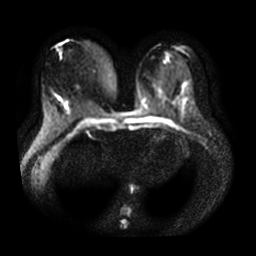
Breast MRI, one axial slice; position 17 of 35 along the scan axis; diffusion-weighted series; image 2 of 4 stored at this slice position (different b-values; order by instance number); 3 T; 5 mm slice thickness; 256 × 256 image matrix. Female patient.
Structures marked on this image (expert manual segmentation):
- tumour on diffusion-weighted imaging: box from (x=64, y=103) to (x=68, y=109) px